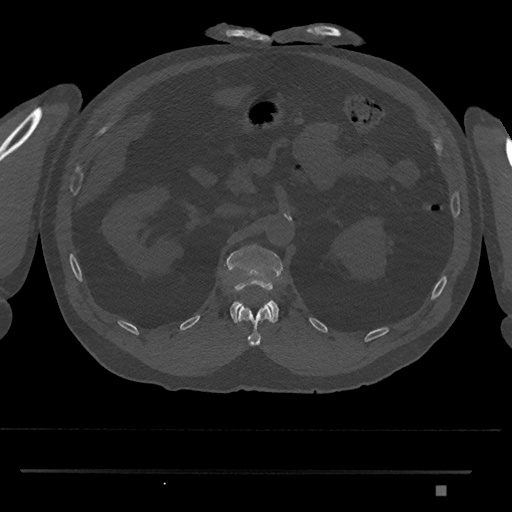
CT including the spine, one axial slice. Slice 855 of 1134 in the series (ordered by position). Reconstruction kernel Br40s/3. Bone window (W 1800 / L 400 HU). 0.5 mm slice thickness. 512 × 512 image matrix. Male patient, age 65 years. Case-level facts recorded for this patient, not image findings: primary cancer: prostate.
Outlined on this slice (semi-automatic segmentation, software-assisted and operator-edited):
- L1 vertebra: bounding box (x1, y1, x2, y2) in pixels: (224, 244, 284, 324)
- T12 vertebra: (237, 303, 273, 346)